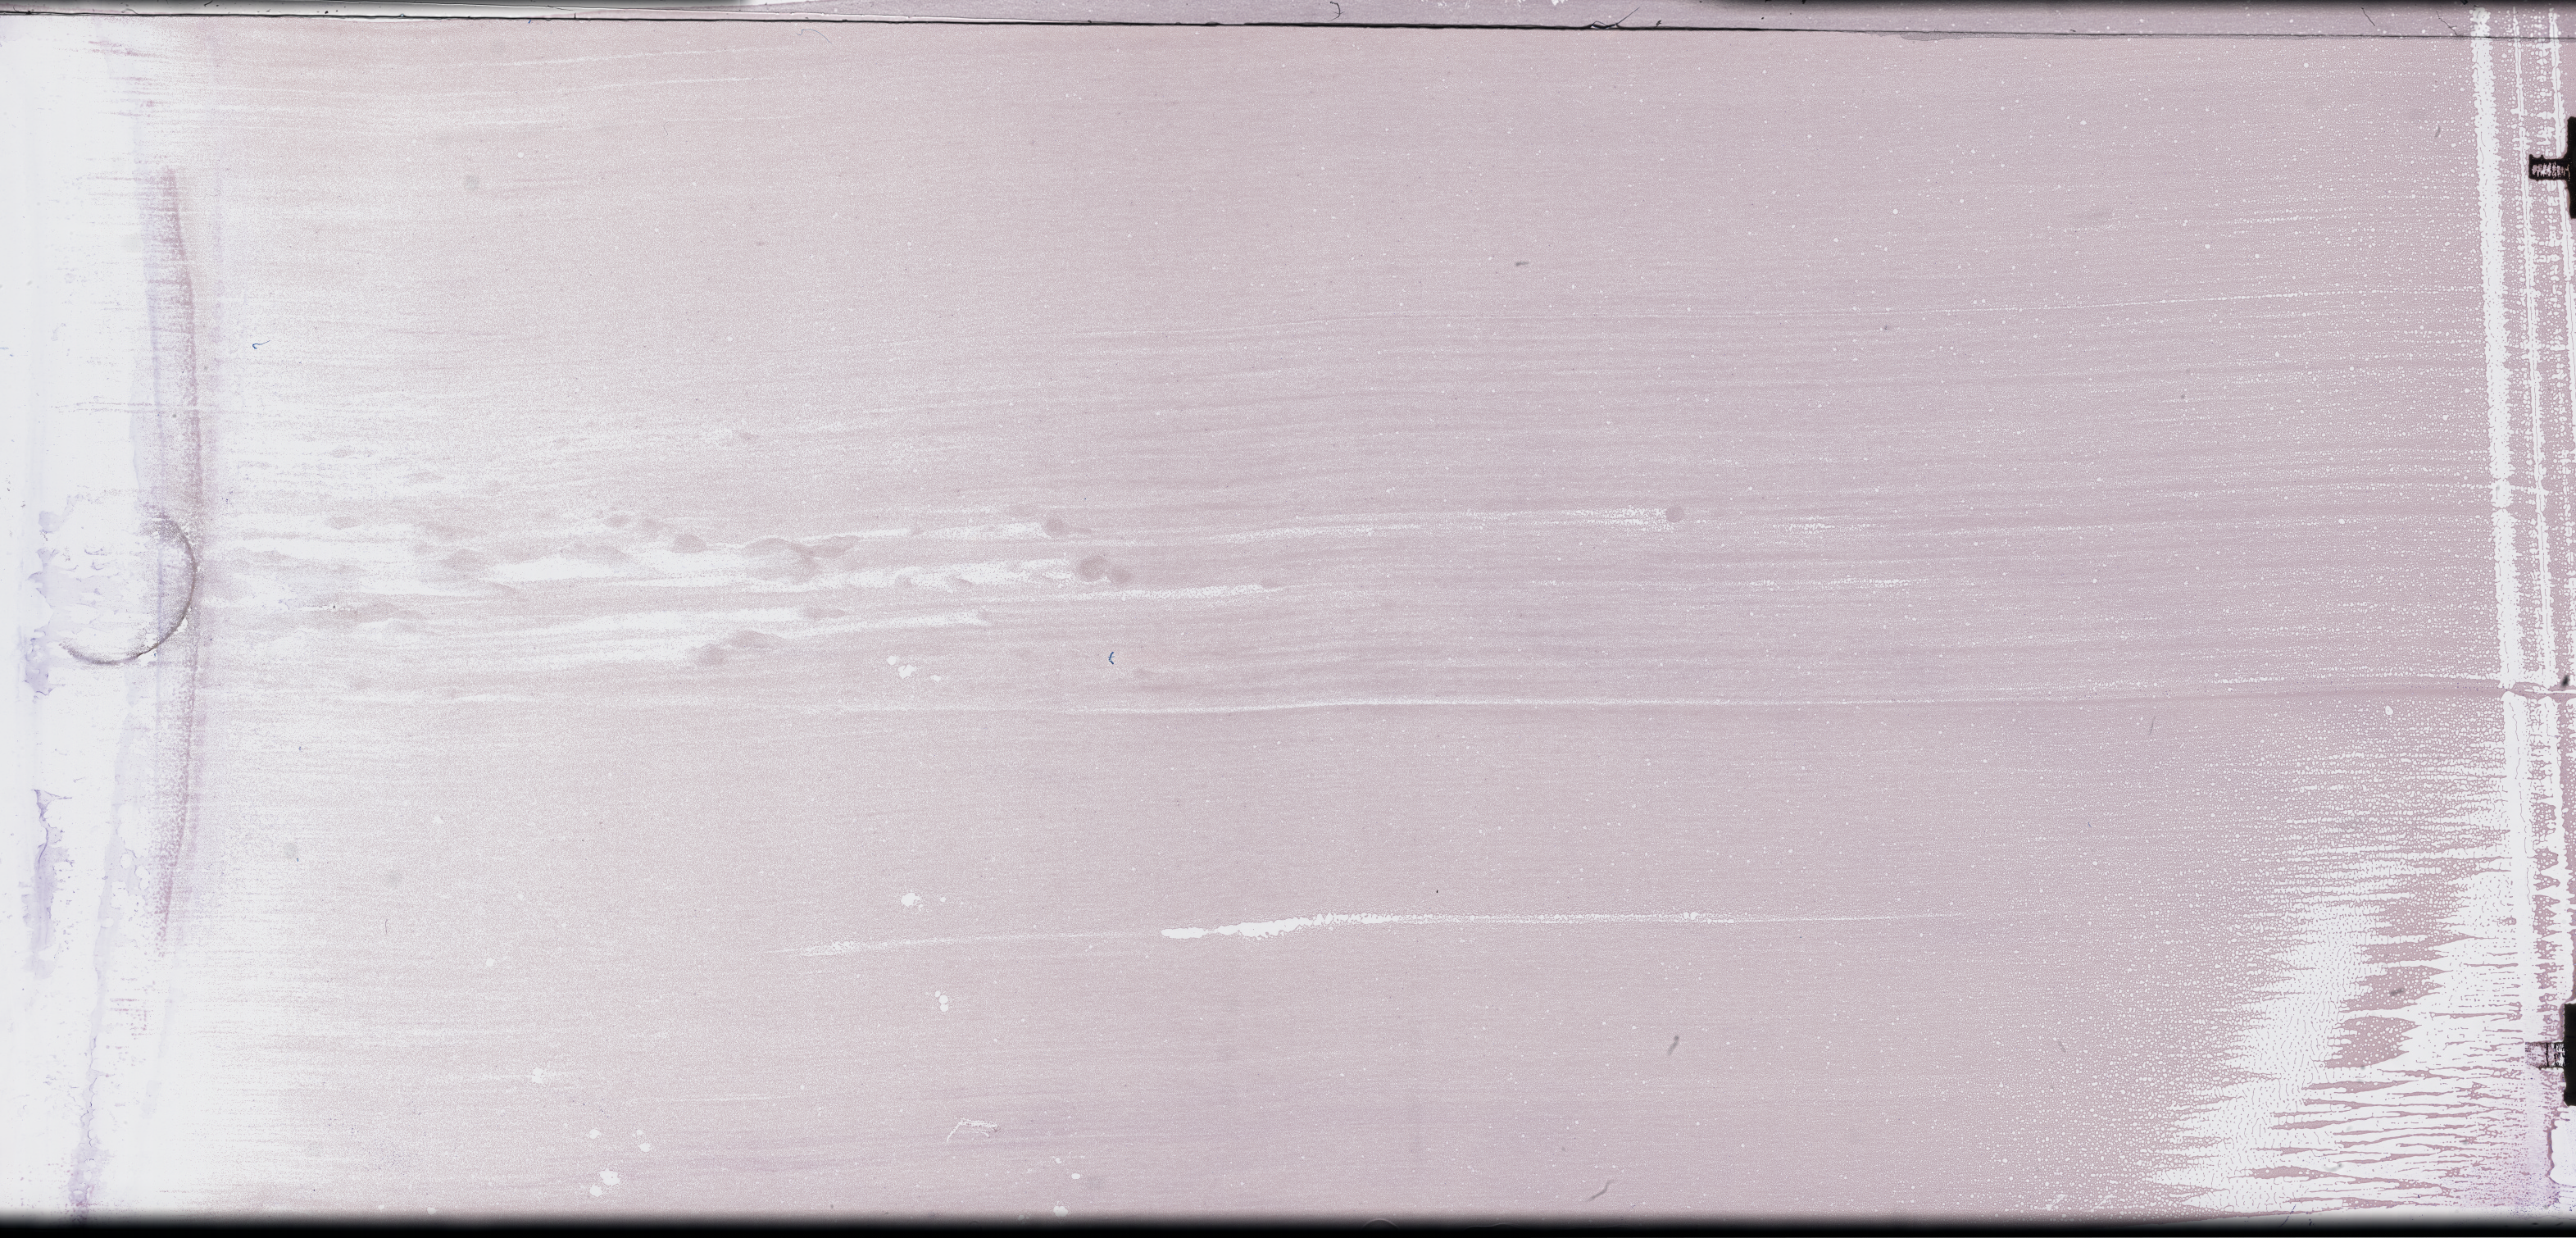
Whole-slide image of a whole blood smear, Wright–Giemsa stain — low-resolution overview of the scanned area, about 50.8 x 24.4 mm. EDTA-anticoagulated smear. Patient sex: male.
Patient diagnosis: Plasma Cell Myeloma.